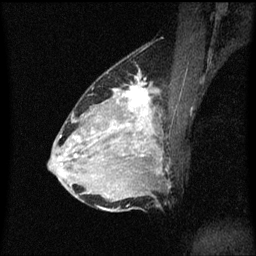
Breast MRI (dynamic contrast-enhanced), one sagittal slice. Position 34 of 60 along the scan axis. Dynamic contrast-enhanced series, image 2 of 3 at this slice position (ordered by acquisition). 1.5 T. TE 4.2 ms, TR 8.4 ms. 2 mm slice thickness. 256 × 256 image matrix, field of view 200 × 200 mm. Female patient, age 34 years. Case-level facts recorded for this patient, not image findings: setting: breast cancer imaged before/during neoadjuvant chemotherapy; receptor status: HR-positive, HER2-negative.
Outlined on this slice (semi-automatically segmented with operator editing):
- analysis volume of interest (the breast-tissue region the enhancement analysis was run in; not a lesion): bounding box <69,70,172,209> (left, top, right, bottom; pixels)
- tumour enhancement mask (voxels above the 70 % enhancement threshold inside the analysis volume of interest): <74,84,161,173>